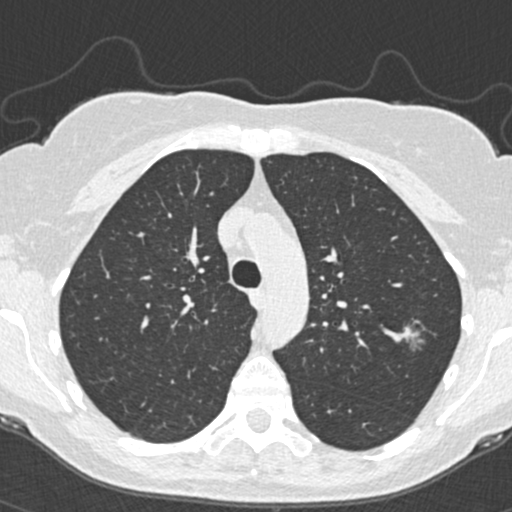
Low-dose screening chest CT, one axial slice; position 262 of 350 along the scan axis; reconstruction kernel B30f; lung window (W 1500 / L -600 HU); 1 mm slice thickness; 512 × 512 image matrix, field of view 298 × 298 mm.
Annotated regions visible in this slice (outlined manually by an expert reader):
- lesion 1 (tumor, upper lobe of left lung): bounding box (x1, y1, x2, y2) in pixels: (399, 326, 425, 350)